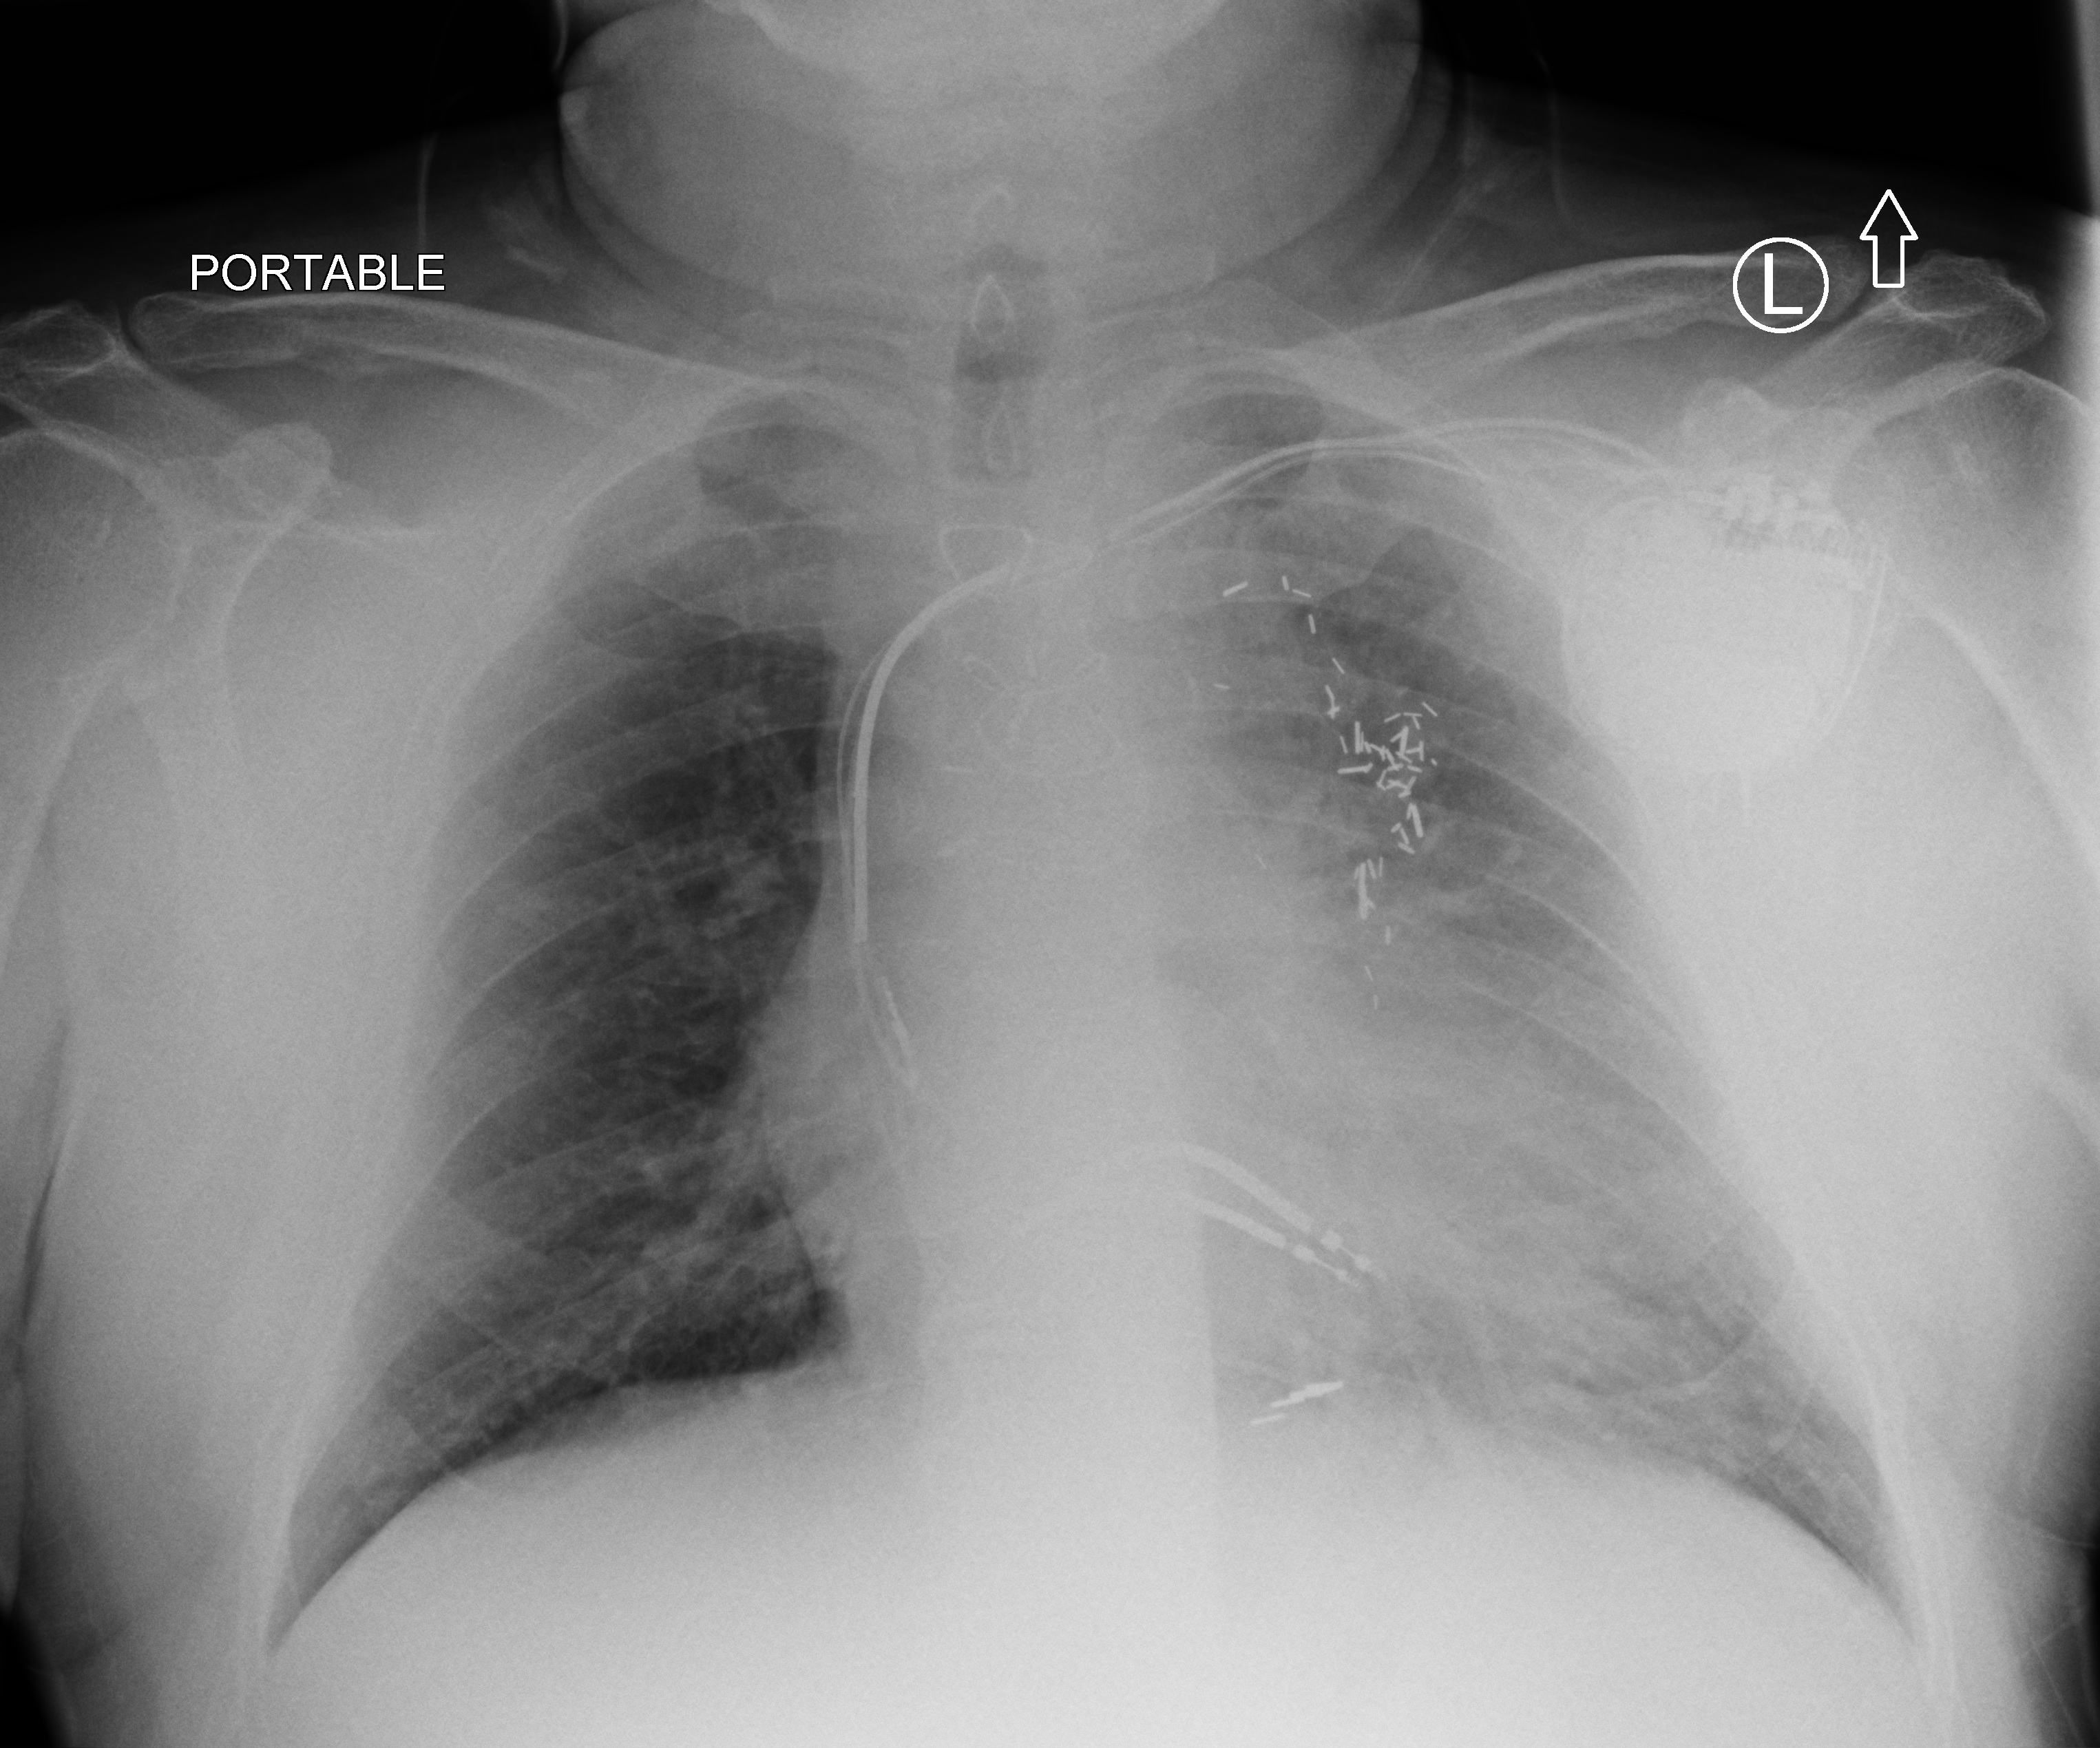
Portable chest radiograph; anteroposterior (AP) projection. Male patient hospitalised with COVID-19, age 60–74 years.
From the hospital-stay record, not from the radiograph (when in the stay this image was taken is not recorded): mechanically ventilated during this hospital stay: yes; length of hospital stay: 55 days.